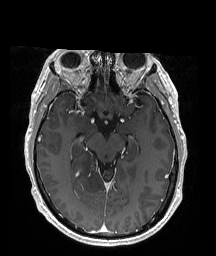
Brain MRI from a brain-tumour surgery series, one axial slice. Position 110 of 176 along the scan axis. T1-weighted post-contrast. 1 mm slice thickness. 216 × 256 image matrix, field of view 211 × 250 mm. Case-level facts recorded for this patient, not image findings: histopathology: Oligodendroglioma; WHO grade: 2; IDH mutation: yes; tumour location: Right Parietal.
Outlined on this slice (expert manual segmentation):
- tumour: bounding box (x1, y1, x2, y2) in pixels: (70, 150, 111, 205)